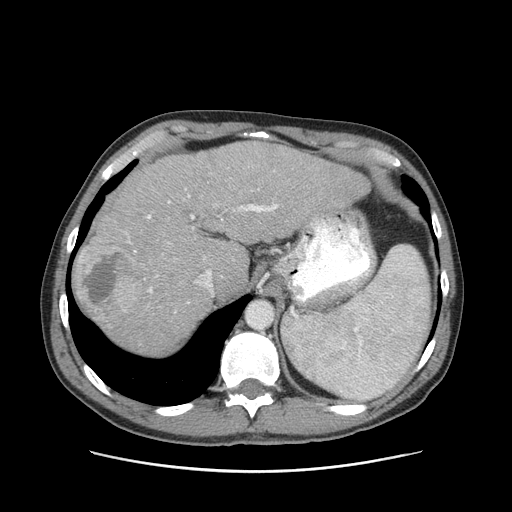
Contrast-enhanced abdominal CT (liver protocol), one axial slice; position 73 of 93 along the scan axis; reconstruction kernel STANDARD; 120 kVp; soft-tissue window (W 400 / L 40 HU); 512 × 512 image matrix, field of view 380 × 380 mm. From the clinical record (not read from this slice): diagnosis: hepatocellular carcinoma (patient treated with transarterial chemoembolisation; whether this scan precedes or follows treatment is not stated here); TNM stage (as recorded): Stage-II; Child-Pugh class: A; tumour differentiation: moderately differentiated; tumour nodularity: multinodular.
Outlined on this slice (semi-automatically segmented with operator editing):
- abdominal aorta: bounding box [x1, y1, x2, y2] px = [247, 301, 271, 327]
- liver parenchyma outside the tumour (the mass and vessels are separate outlines, so this box may not span the whole liver): [74, 140, 368, 354]
- mass: [77, 239, 145, 327]
- liver vessels: [134, 189, 278, 303]